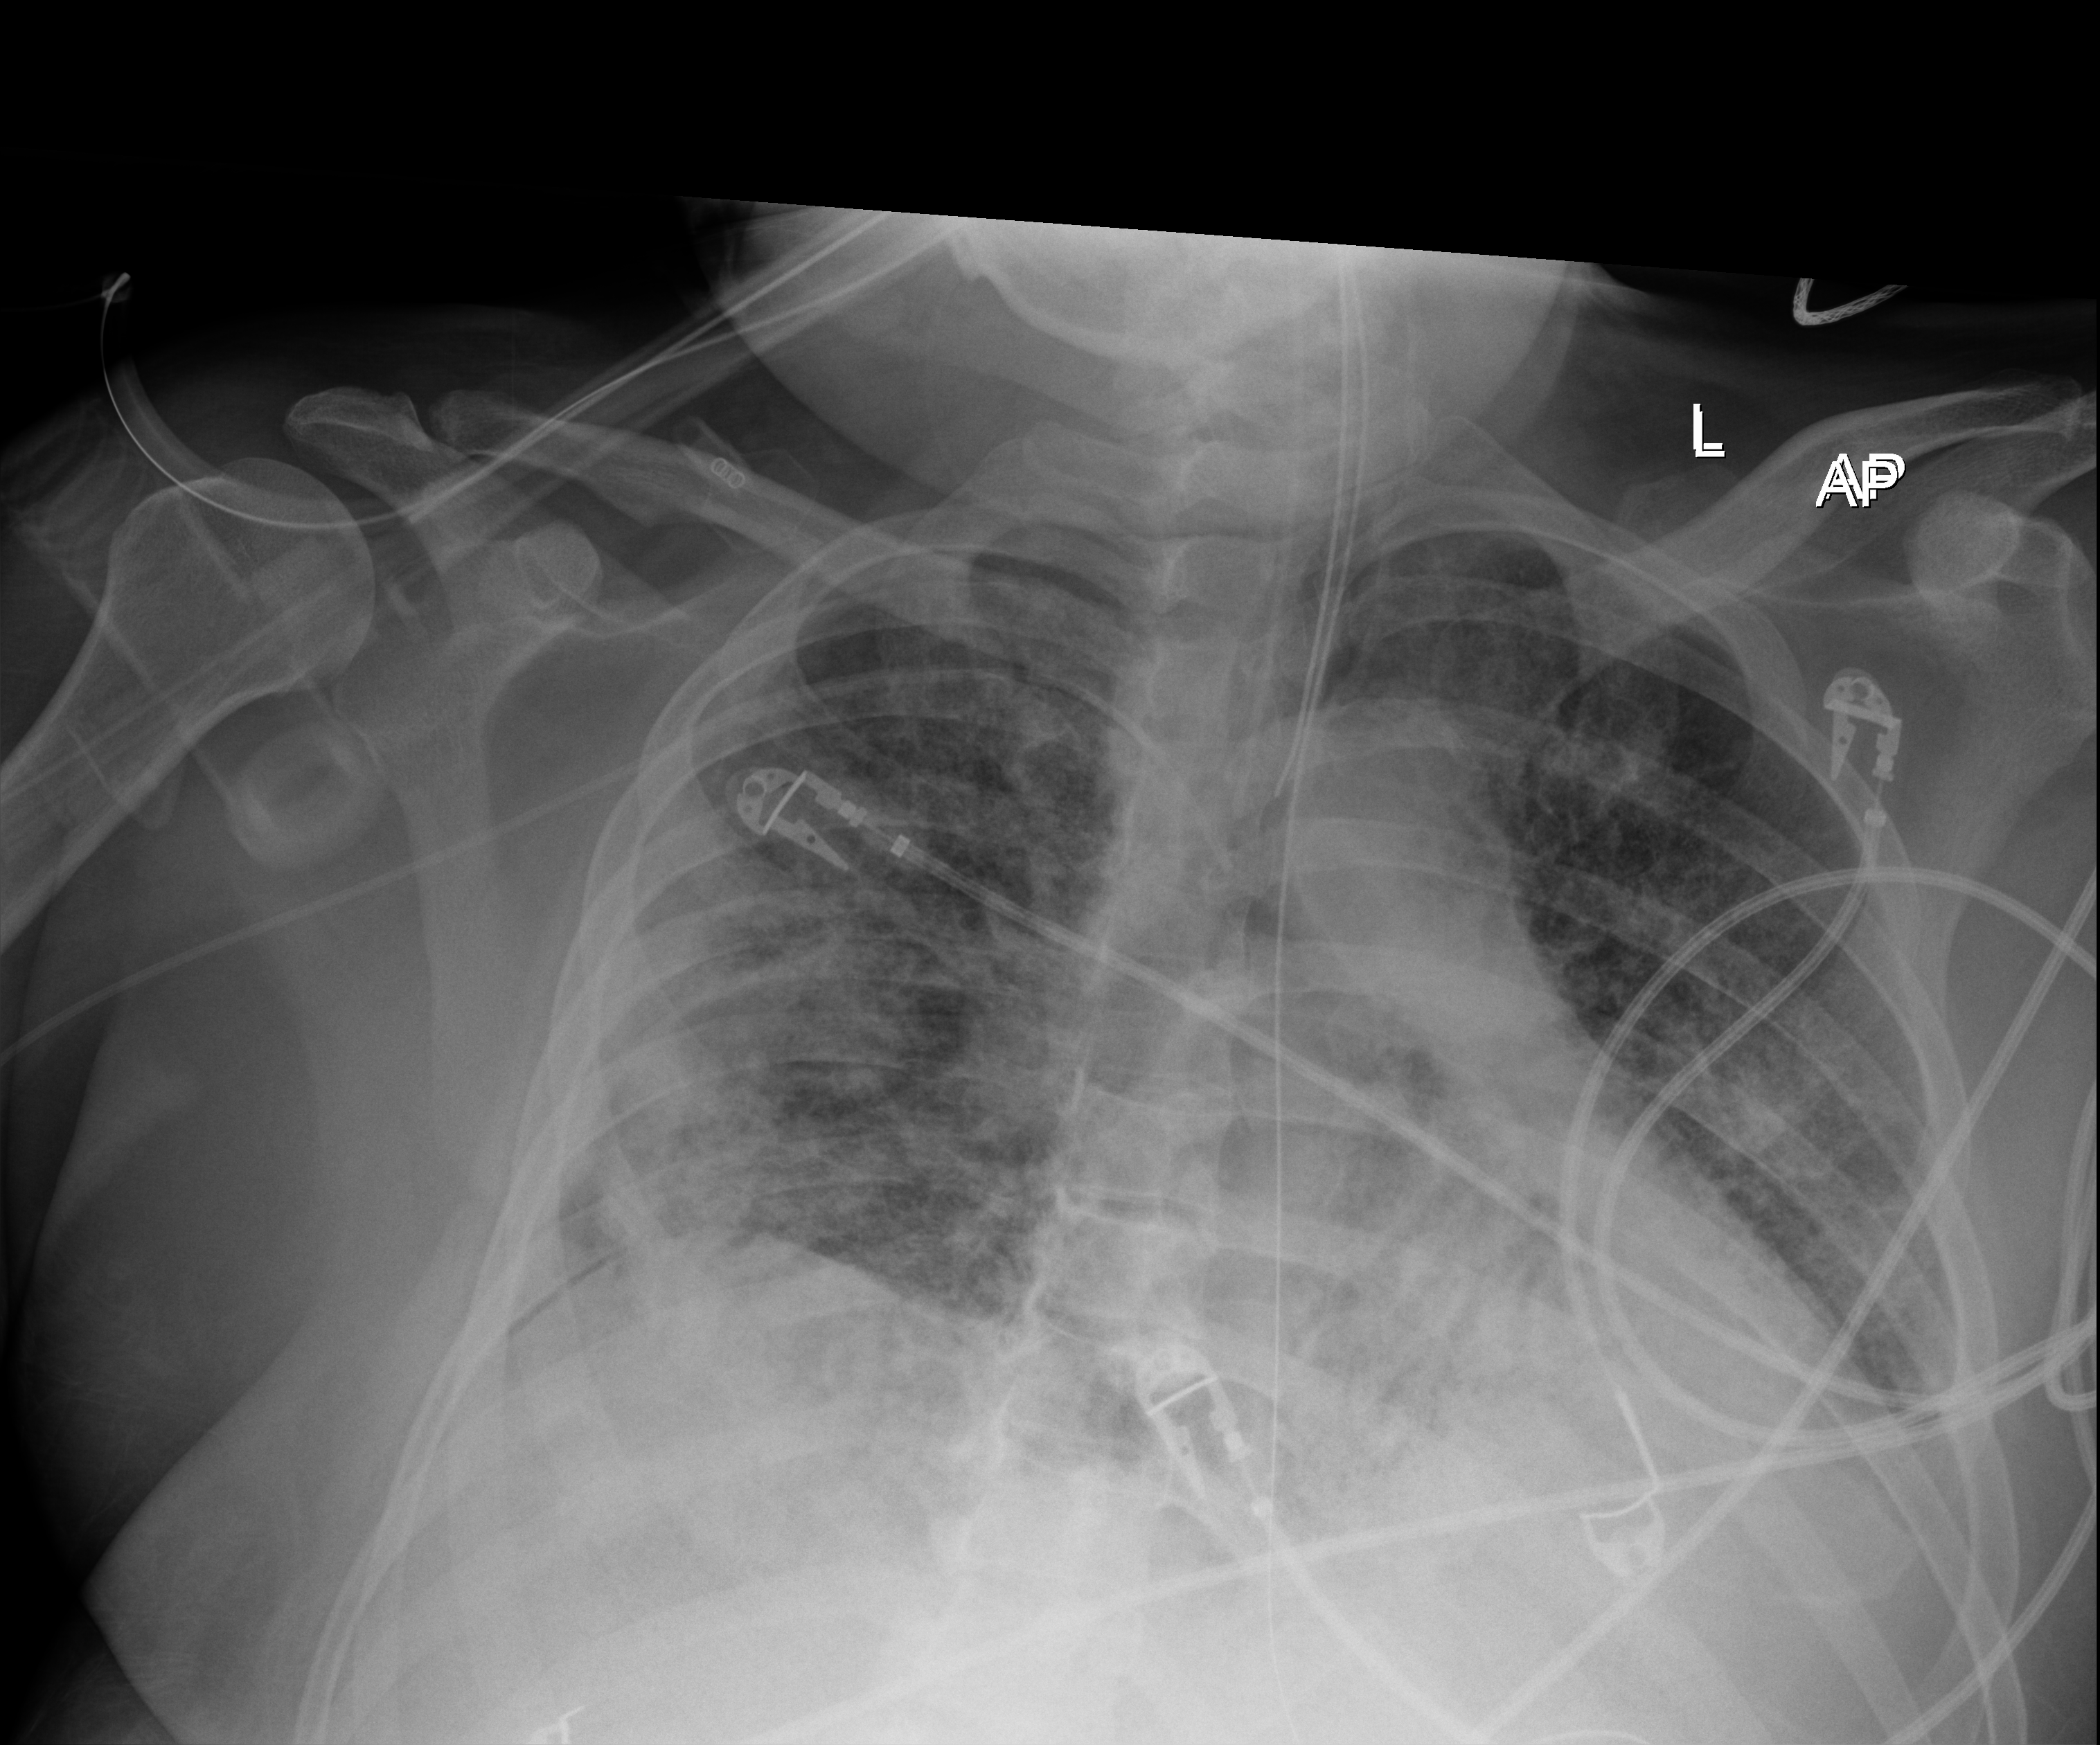
Chest X-ray (portable); anteroposterior (AP) projection. Patient hospitalised with COVID-19; male, aged 18–59 years.
From the hospital-stay record, not from the radiograph (when in the stay this image was taken is not recorded): other chronic lung disease (admission record): no; mechanically ventilated during this hospital stay: yes; length of hospital stay: 96 days.